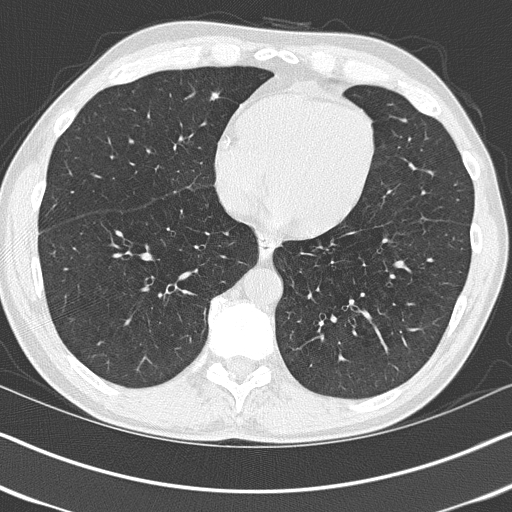
Axial slice from a low-dose chest CT screening exam. Baseline screening round. Lung window (W 1500 / L -600 HU). Lung (sharp) reconstruction kernel (B50f). Slice 105 of 151 in the series. 512 × 512 image matrix, field of view 330 × 330 mm. Male, age 58 years at enrolment.
• Expert-annotated lung lesion, bounding box <189,76,237,121> (left, top, right, bottom; pixels).
• Screening reader's record for this exam (one nodule recorded; not confirmed to be the boxed lesion): non-calcified nodule or mass ≥4 mm, right middle lobe, 5 × 5 mm, soft tissue attenuation.
• Participant outcome: lung cancer diagnosed 421 days after this screen — adenocarcinoma, NOS, right middle lobe, moderately differentiated (G2), stage IIA (AJCC 6th edition), 10 mm at pathology.